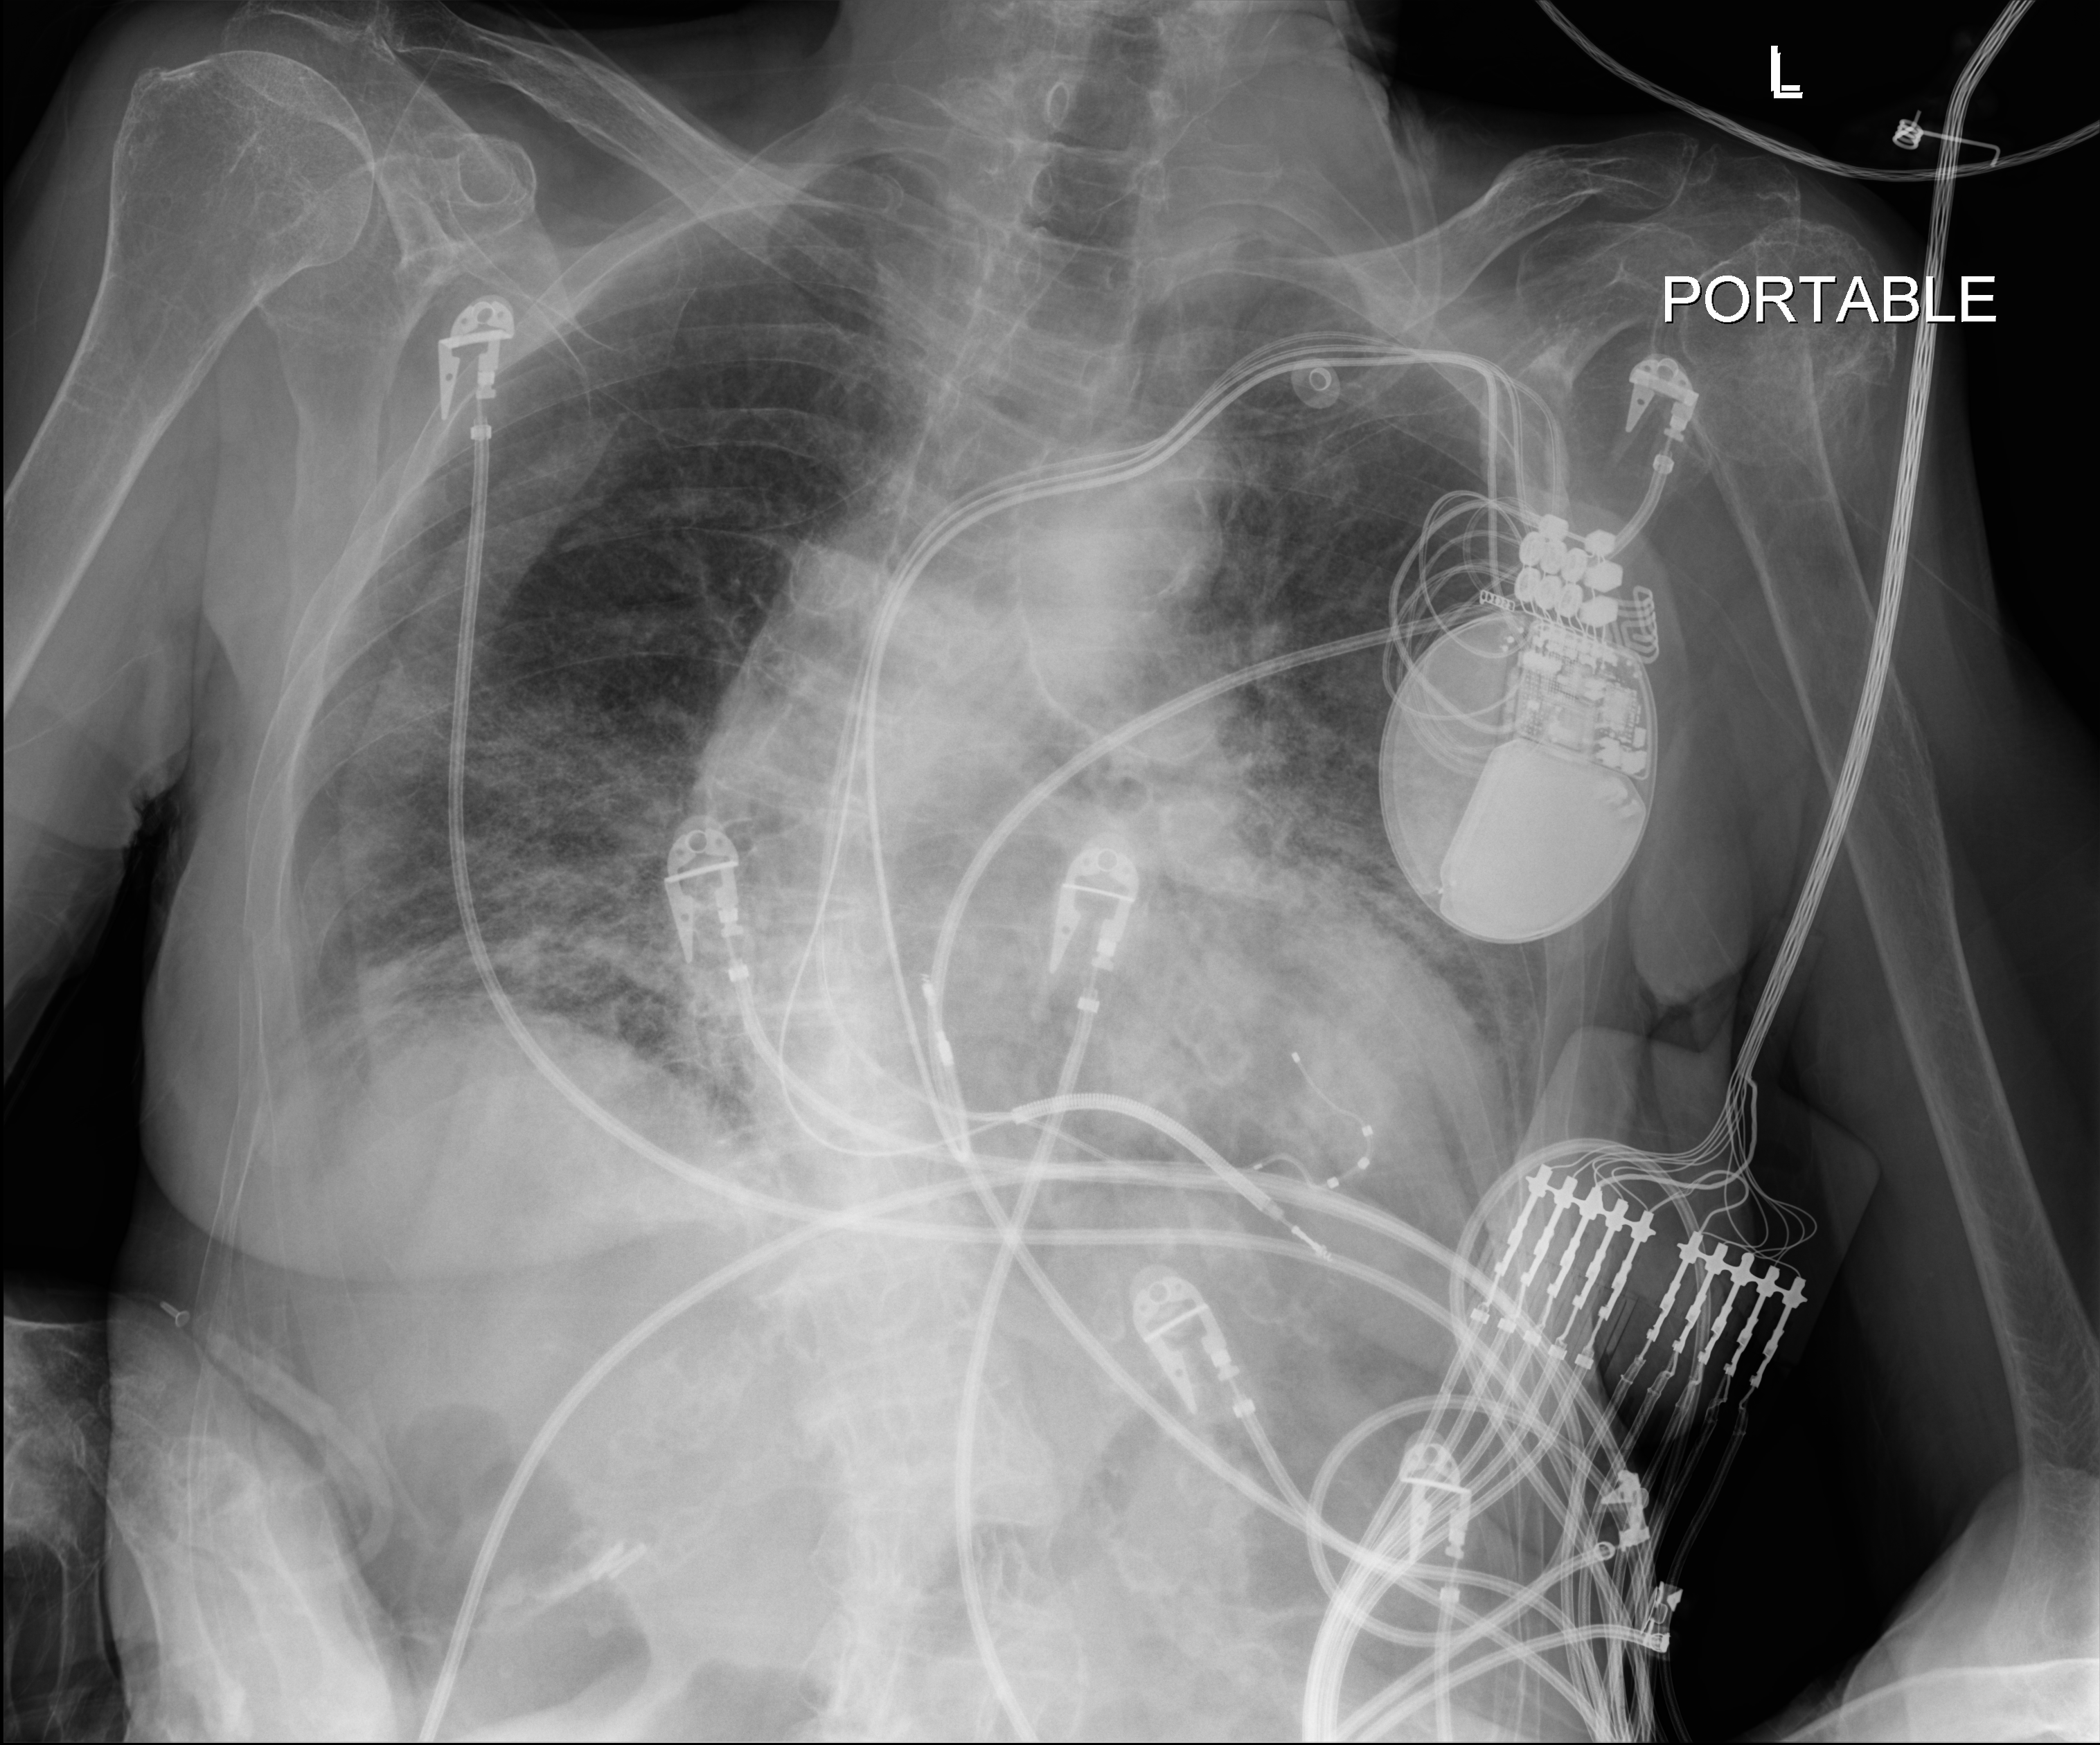
Chest radiograph. Female patient hospitalised with COVID-19, age 75–90 years.
Admission-level facts for this patient (not findings on this image; timing relative to this image not recorded):
- length of hospital stay: 3 days
- chronic kidney disease (admission record): no
- mechanically ventilated during this hospital stay: no